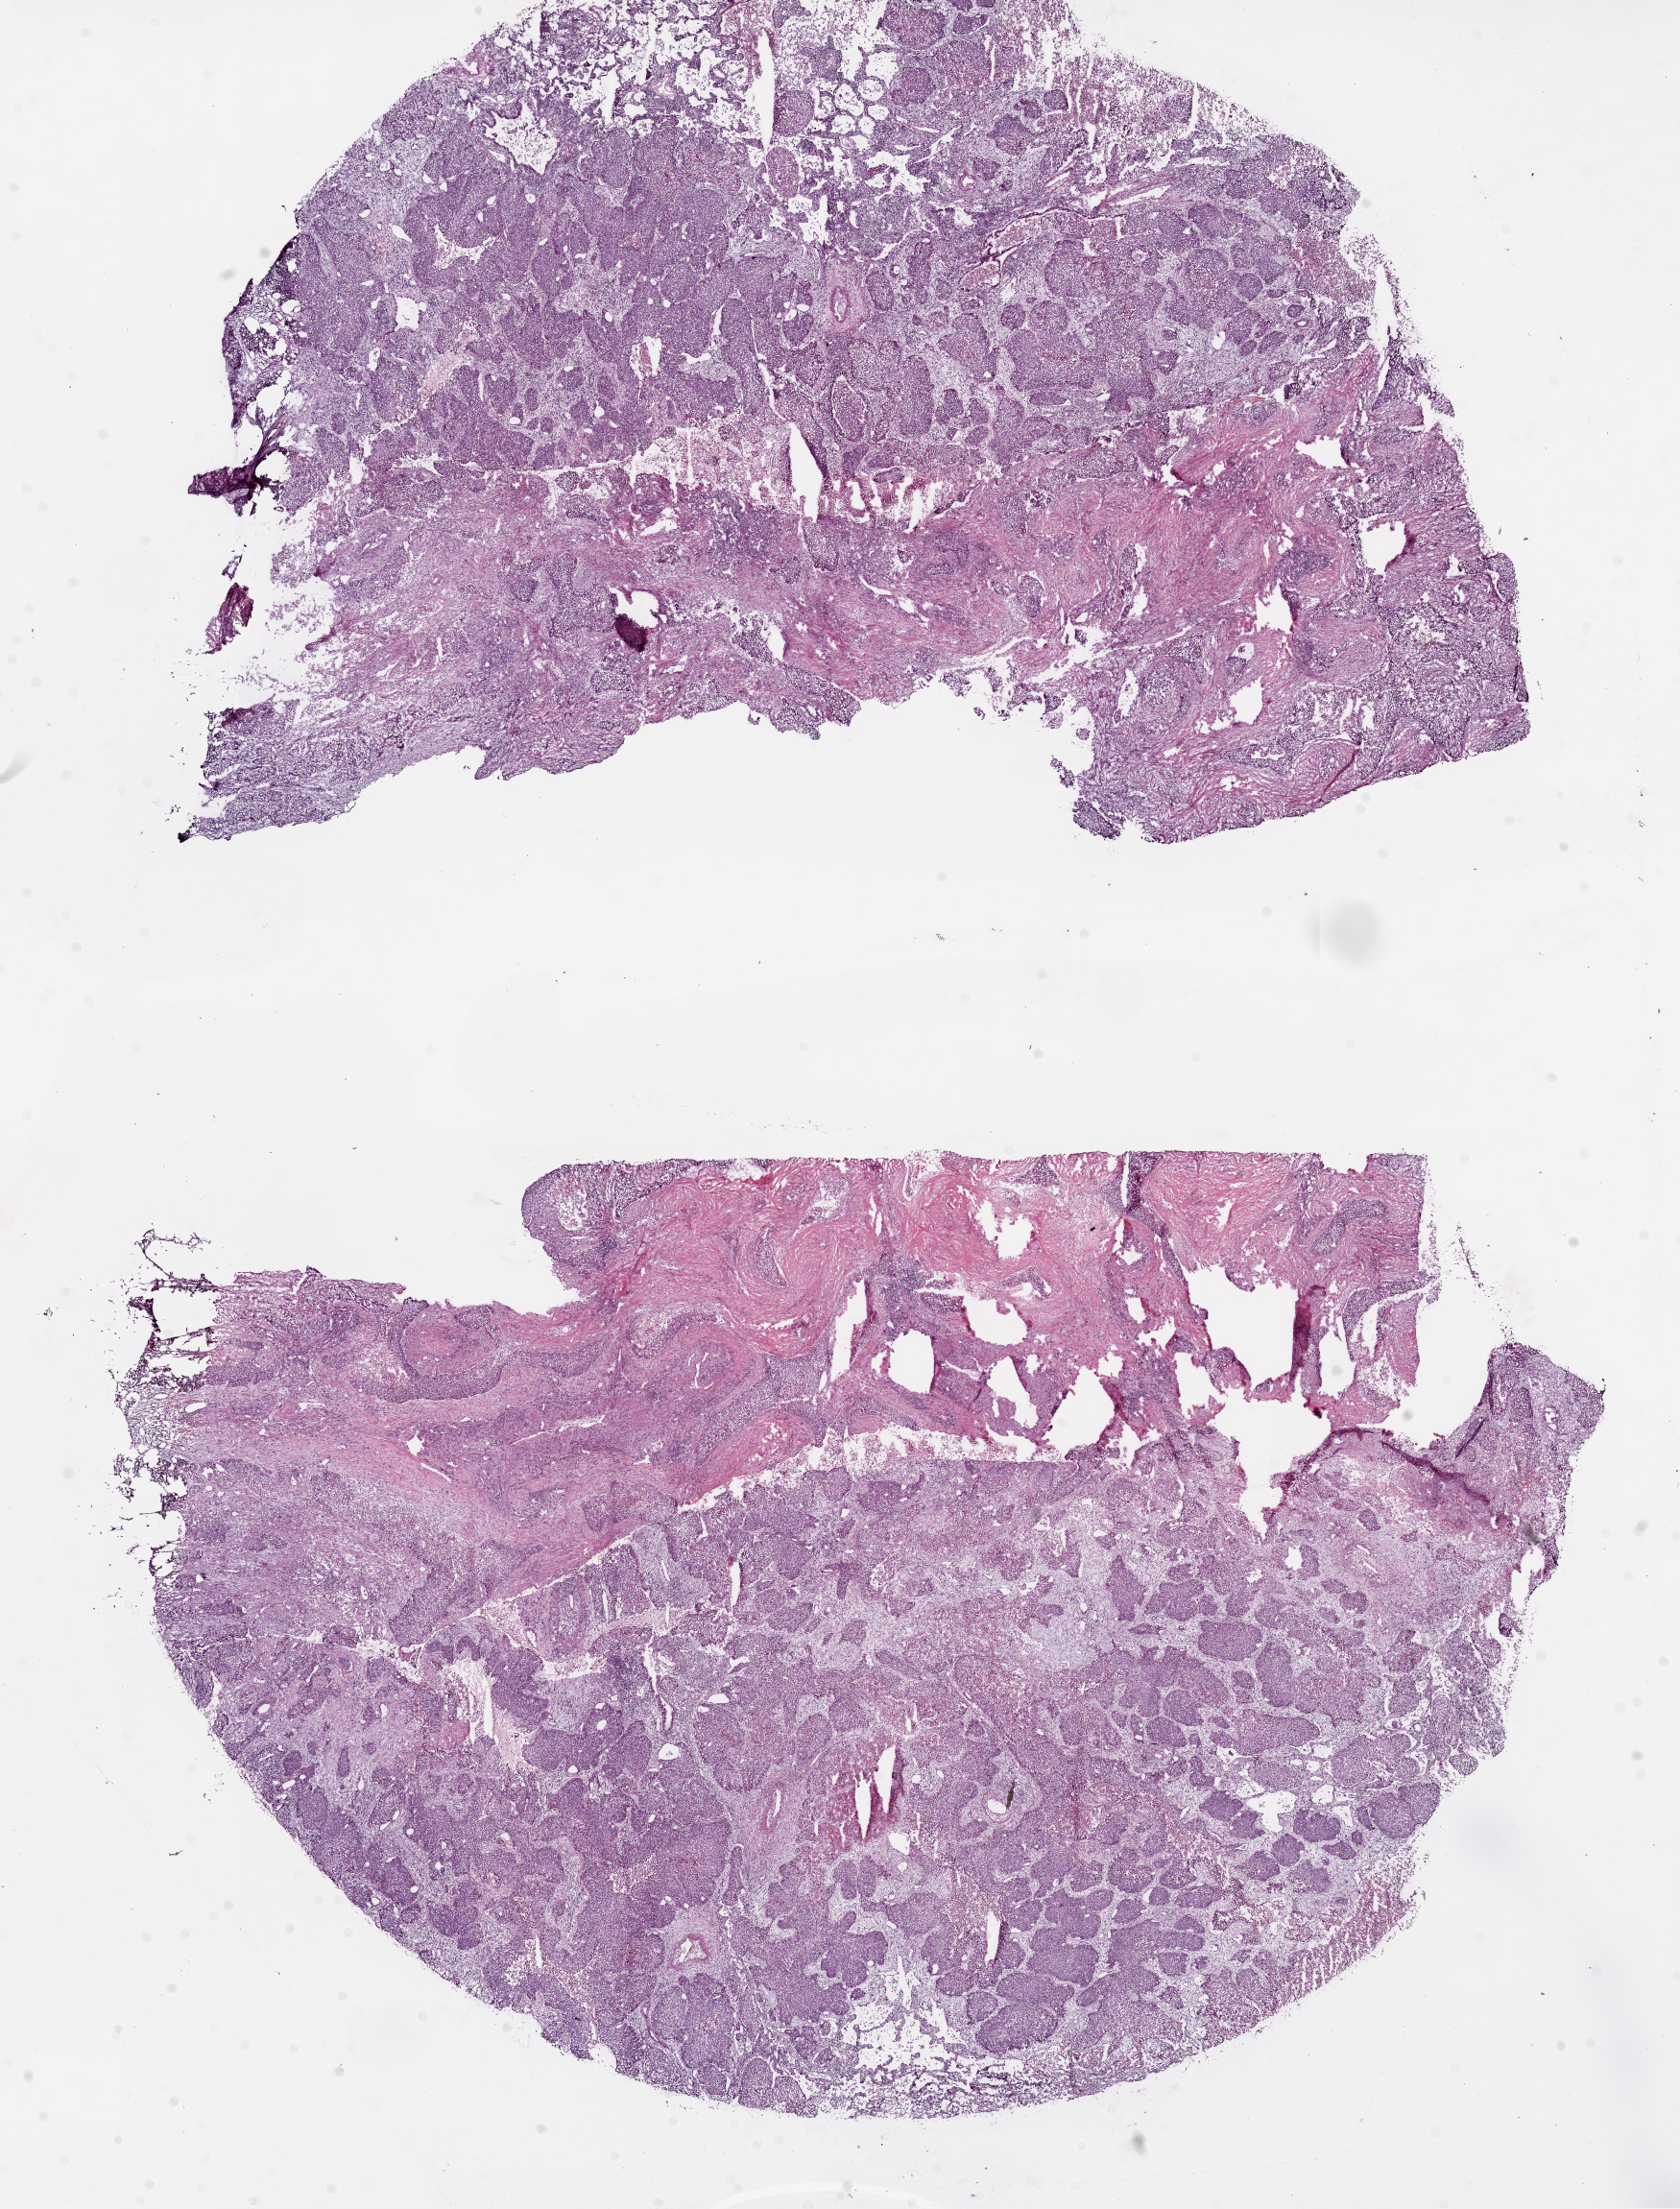
Whole-slide histology image, Hematoxylin and eosin (H&E) stained — a low-resolution overview of the entire scanned area, about 14.0 x 18.5 mm (acquisition: 20x scan), frozen section from the bottom of the tissue portion, sample: primary tumour, lung. Patient: male, age at initial diagnosis 68 years. Slide review estimates, as recorded: tumour cells 55%, tumour nuclei 70%, normal cells 10%, stromal cells 30%, necrosis 5%.
- laterality: right
- AJCC pathologic stage: IB
- histologic diagnosis: Squamous cell carcinoma, NOS